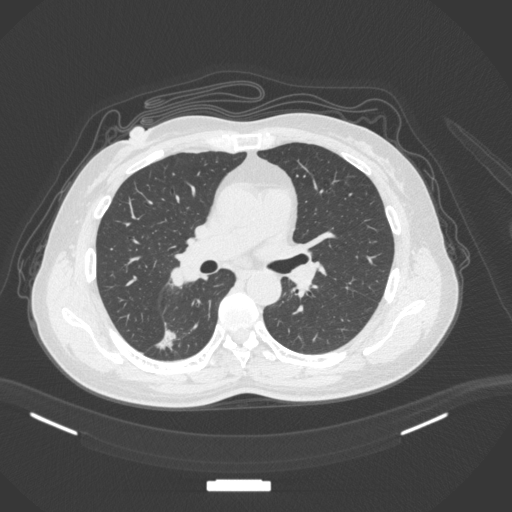
Chest CT, one axial slice. 120 kVp. Lung window (W 1500 / L -600 HU). 1 mm slice thickness. 512 × 512 image matrix. Patient: female, 55 years. Case-level facts recorded for this patient, not image findings: clinical TNM (as recorded): T1c N1 M0.
Structures marked on this image (bounding box drawn by a radiologist):
- lung tumour (recorded histology: adenocarcinoma): box from (x=153, y=327) to (x=180, y=353) px